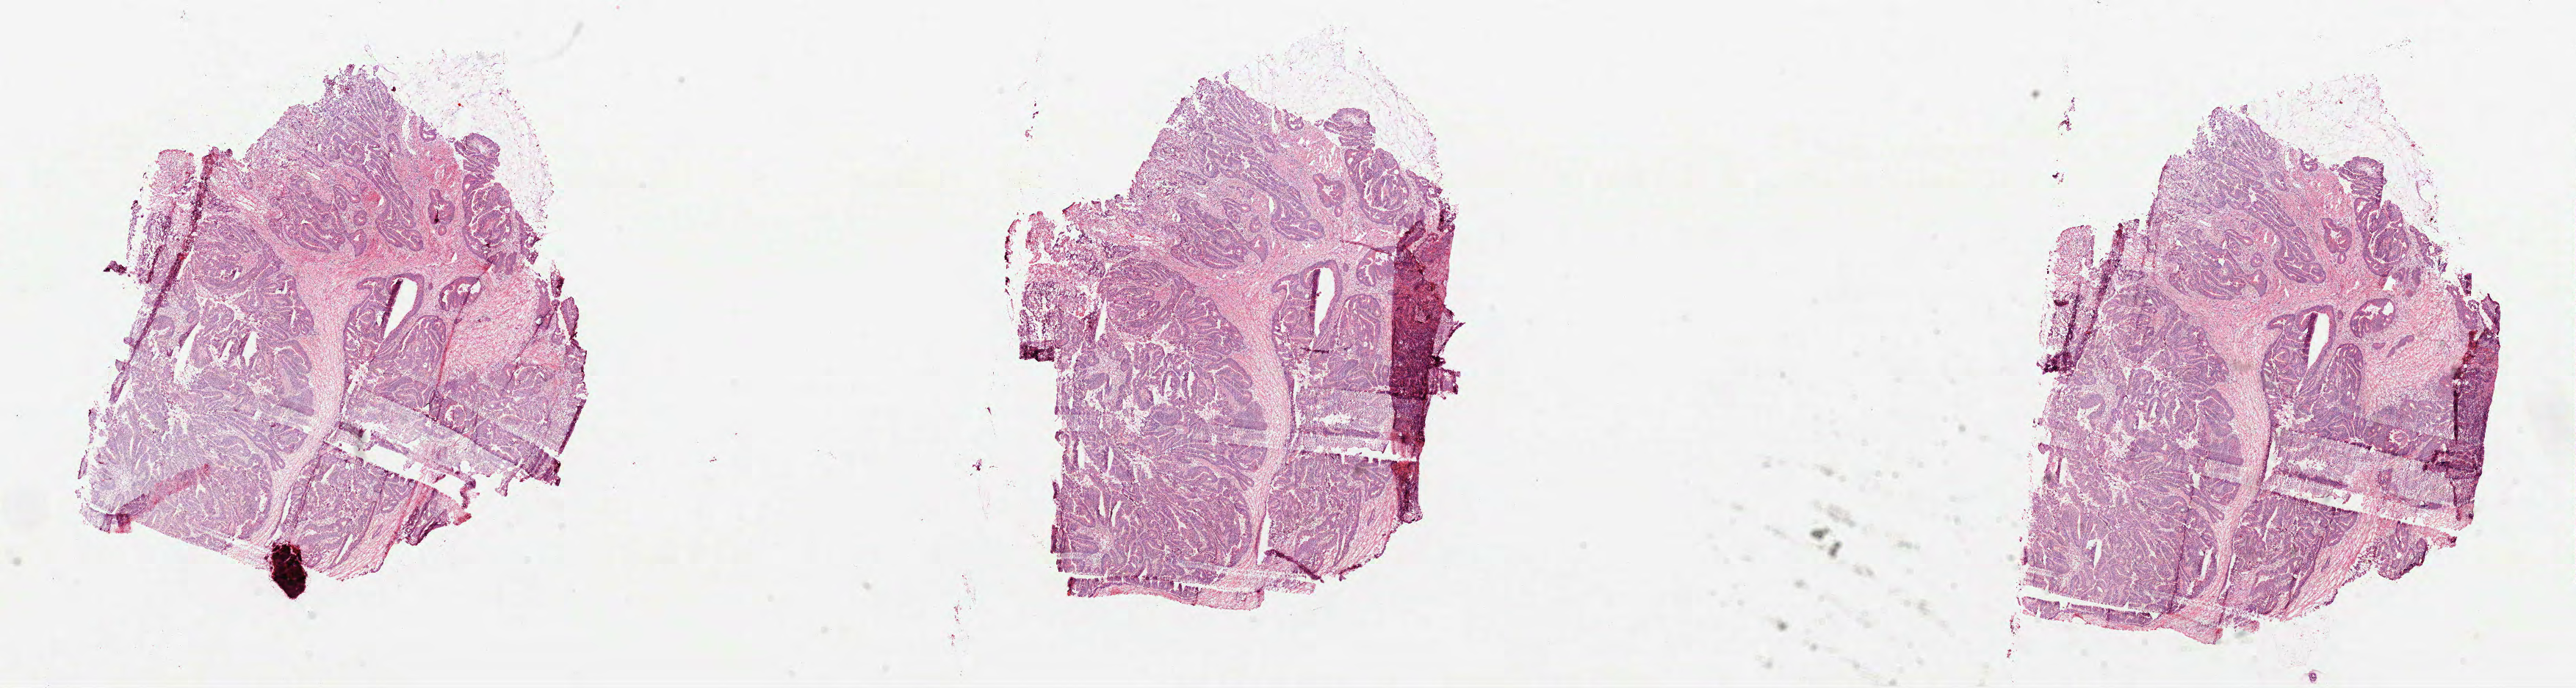
Whole-slide histology image, H&E-stained — shown as a low-resolution overview of the whole scanned area (about 28.3 x 7.6 mm); formalin-fixed paraffin-embedded (FFPE) diagnostic section; sample: primary tumour, rectum. Male, age 58 years at initial diagnosis.
Lymph nodes positive (case pathology): 7 of 13 examined. Diagnosis: Tubular adenocarcinoma. AJCC pathologic stage: IV.